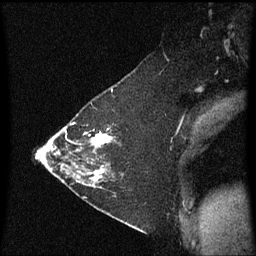
Breast MRI (dynamic contrast-enhanced), one sagittal slice. Position 41 of 60 along the scan axis. Dynamic contrast-enhanced series, image 2 of 3 at this slice position (ordered by acquisition). 1.5 T. TE 4.2 ms, TR 8.4 ms. 2 mm slice thickness. 256 × 256 image matrix, field of view 200 × 200 mm. Female patient, age 36 years. Case-level facts recorded for this patient, not image findings: setting: breast cancer imaged before/during neoadjuvant chemotherapy; receptor status: HR-positive, HER2-negative.
Annotated regions visible in this slice (semi-automatic segmentation, software-assisted and operator-edited):
- analysis volume of interest (the breast-tissue region the enhancement analysis was run in; not a lesion): box from (x=72, y=116) to (x=123, y=187) px
- tumour enhancement mask (voxels above the 70 % enhancement threshold inside the analysis volume of interest): (x=76, y=132)–(x=113, y=183)